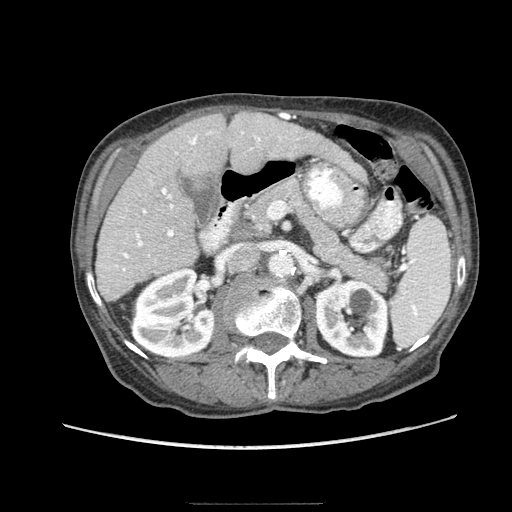
Contrast-enhanced abdominal CT (liver protocol), one axial slice. Slice 38 of 83 in the series (ordered by position). 140 kVp. Soft-tissue window (W 400 / L 40 HU). 2.5 mm slice thickness. 512 × 512 image matrix. From the clinical record (not read from this slice): diagnosis: hepatocellular carcinoma (patient treated with transarterial chemoembolisation; whether this scan precedes or follows treatment is not stated here); TNM stage (as recorded): Stage-I; Child-Pugh class: A; tumour differentiation: moderately differentiated; tumour nodularity: uninodular.
Annotated regions visible in this slice (semi-automatically segmented with operator editing):
- liver parenchyma outside the tumour (the mass and vessels are separate outlines, so this box may not span the whole liver): bounding box <96,112,340,300> (left, top, right, bottom; pixels)
- liver vessels: <115,131,281,271>